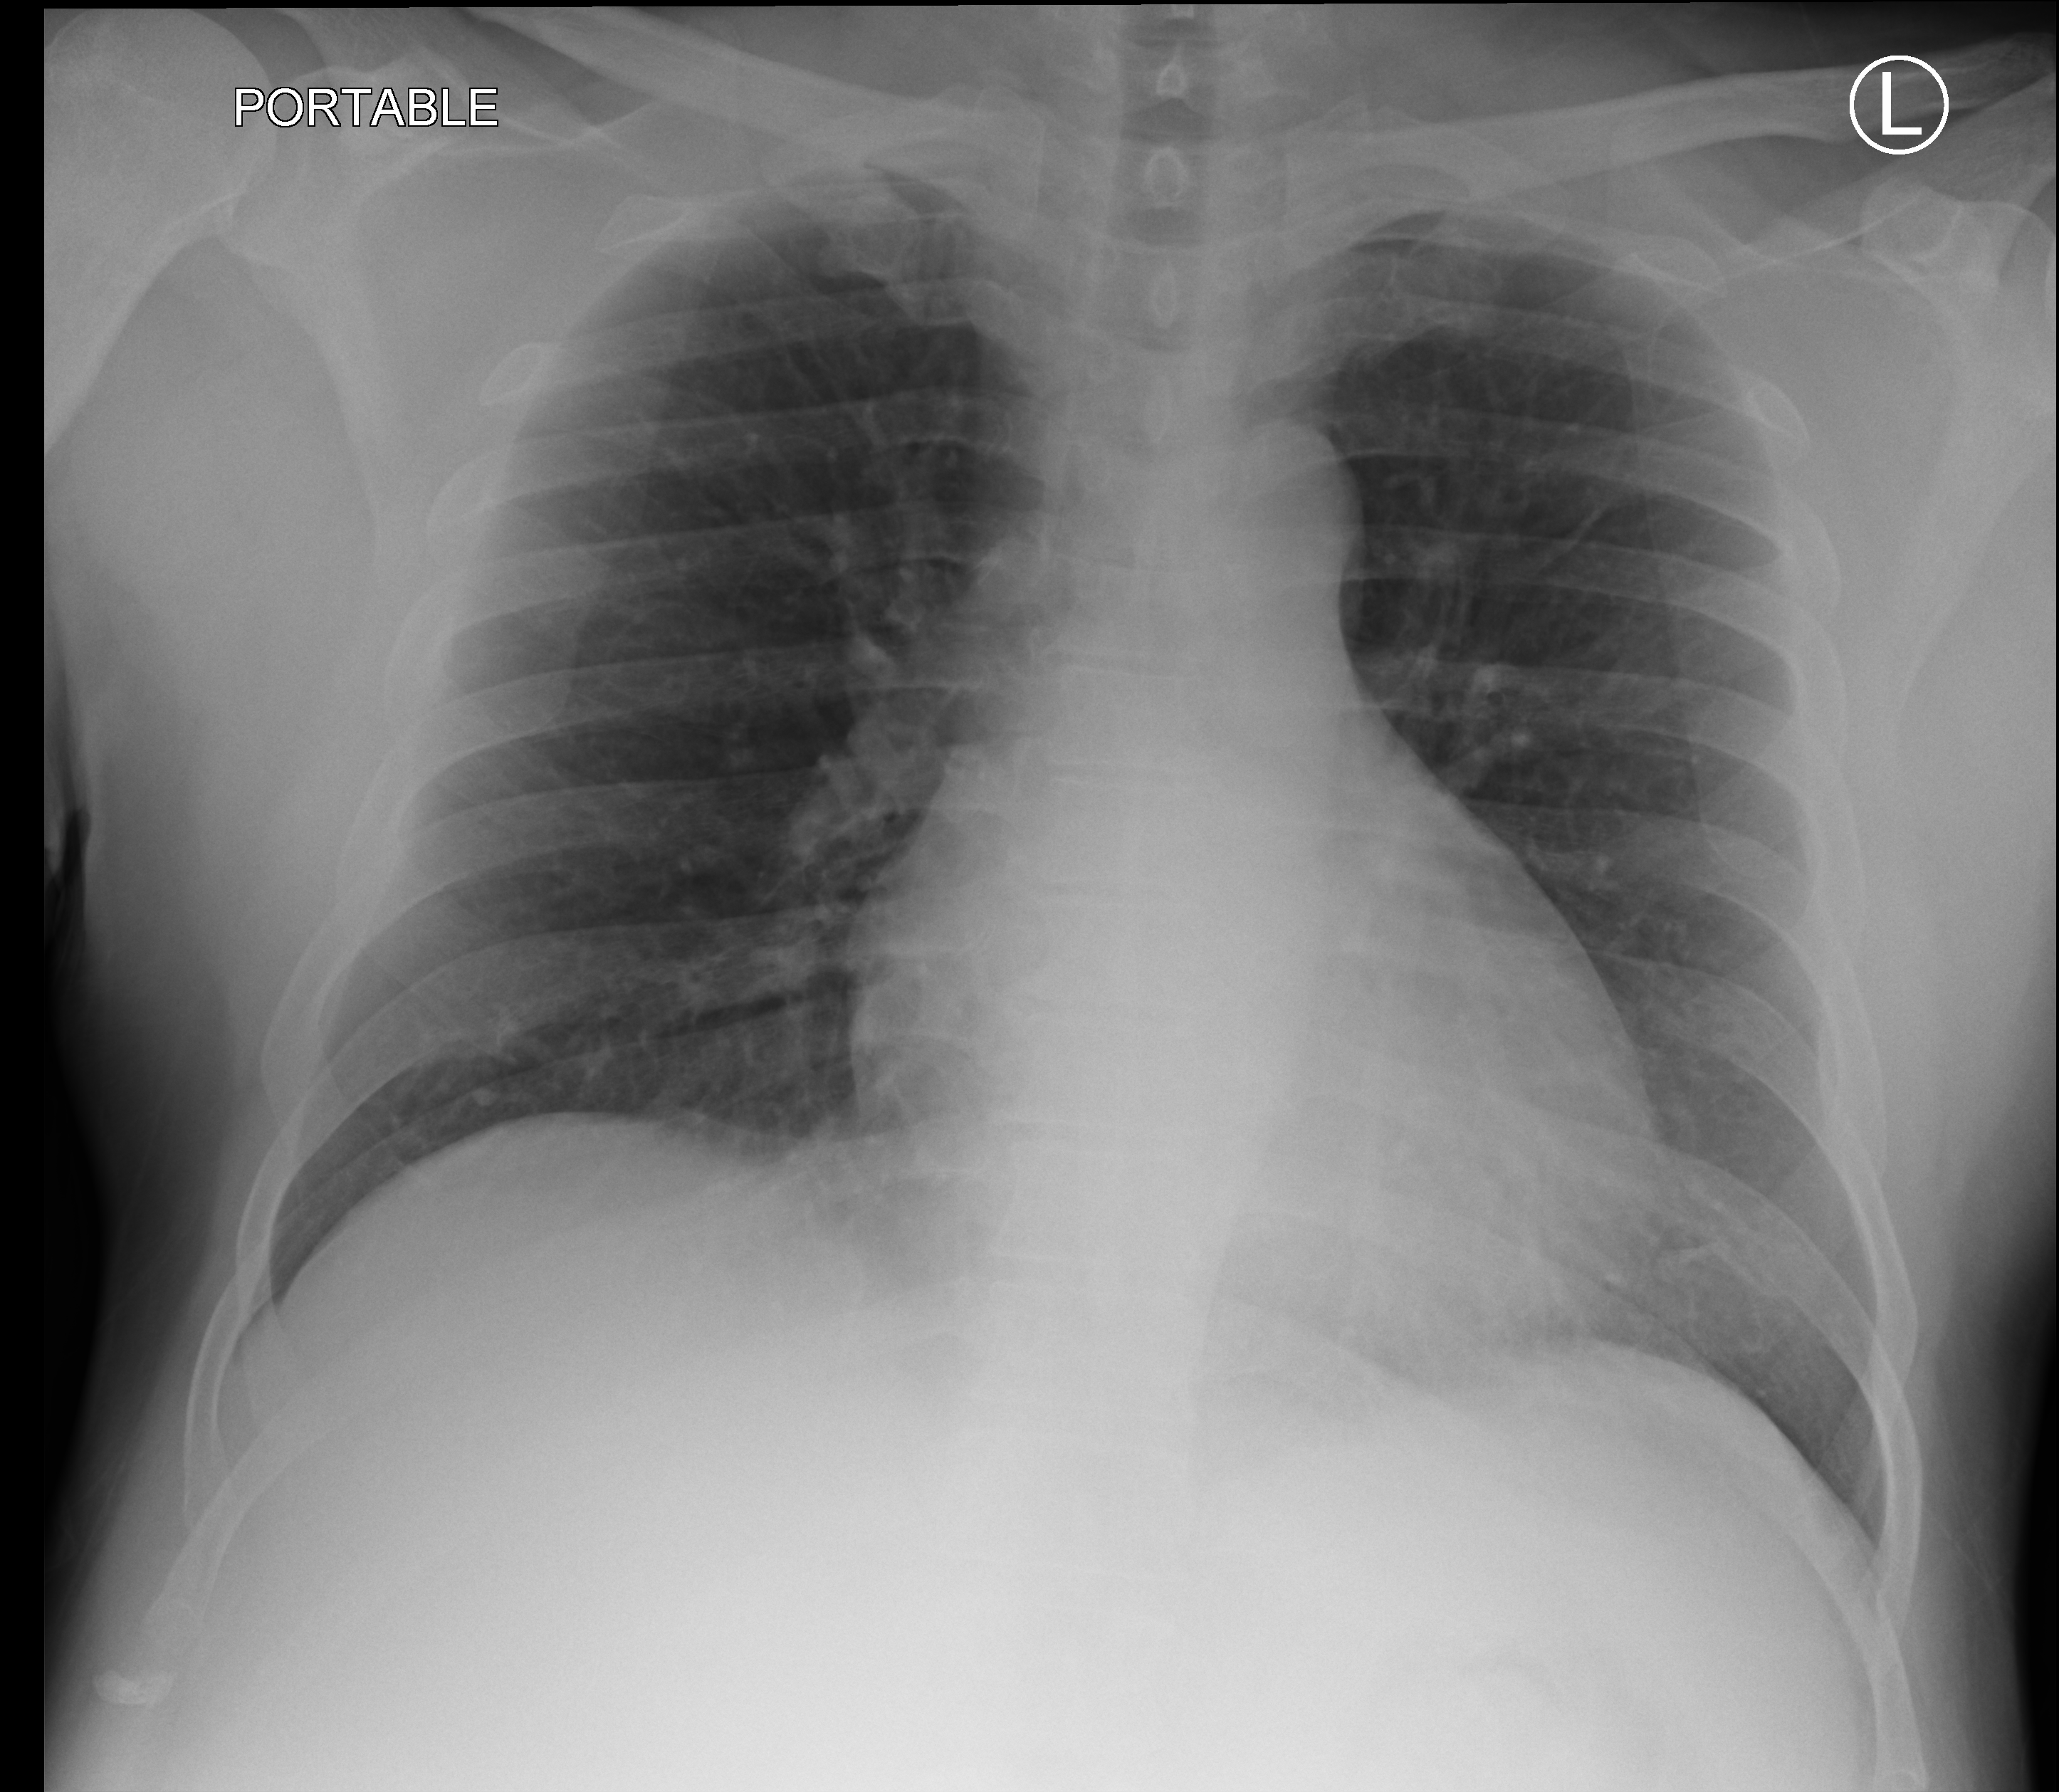
Portable chest radiograph; anteroposterior (AP) projection. Male patient hospitalised with COVID-19, age 18–59 years.
Hospital-stay facts (about this admission, not read from this image; timing relative to this image not recorded):
- smoking status (admission record): never